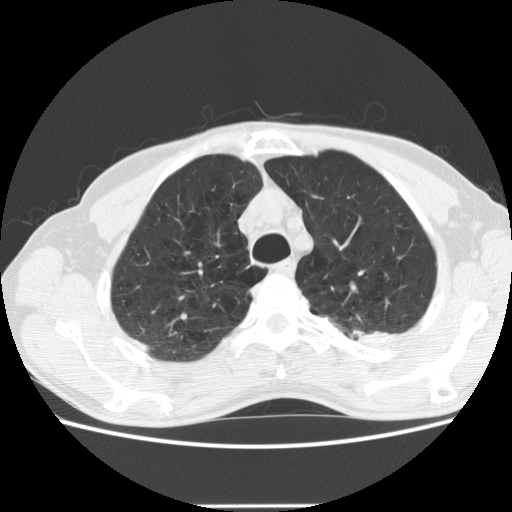
Low-dose screening chest CT, one axial slice; position 156 of 191 along the scan axis; 120 kVp; lung window (W 1500 / L -600 HU); 512 × 512 image matrix, field of view 352 × 352 mm.
Structures marked on this image (expert manual segmentation):
- lesion 1 (tumor, upper lobe of left lung): bounding box <352,330,389,341> (left, top, right, bottom; pixels)